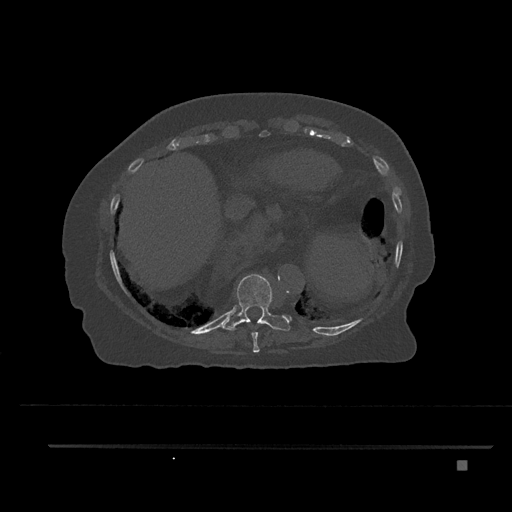
CT including the spine, one axial slice. Position 366 of 797 along the scan axis. 120 kVp. Bone window (W 1800 / L 400 HU). 0.5 mm slice thickness. 512 × 512 image matrix, field of view 437 × 437 mm. Female patient, age 76 years. Case-level facts recorded for this patient, not image findings: primary cancer: lung.
Outlined on this slice (semi-automatic segmentation, software-assisted and operator-edited):
- T10 vertebra: box from (x=219, y=274) to (x=290, y=331) px
- T9 vertebra: (x=251, y=332)–(x=260, y=353)